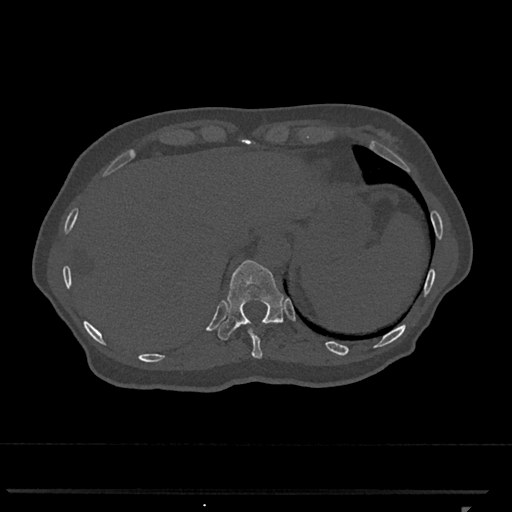
CT including the spine, one axial slice; position 535 of 793 along the scan axis; reconstruction kernel Br40s/3; bone window (W 1800 / L 400 HU); 512 × 512 image matrix. Patient: female, 62 years. From the clinical record (not read from this slice): primary cancer: renal.
Annotated regions visible in this slice (semi-automatically segmented with operator editing):
- T10 vertebra: bounding box <249,329,263,359> (left, top, right, bottom; pixels)
- T11 vertebra: <218,260,285,340>